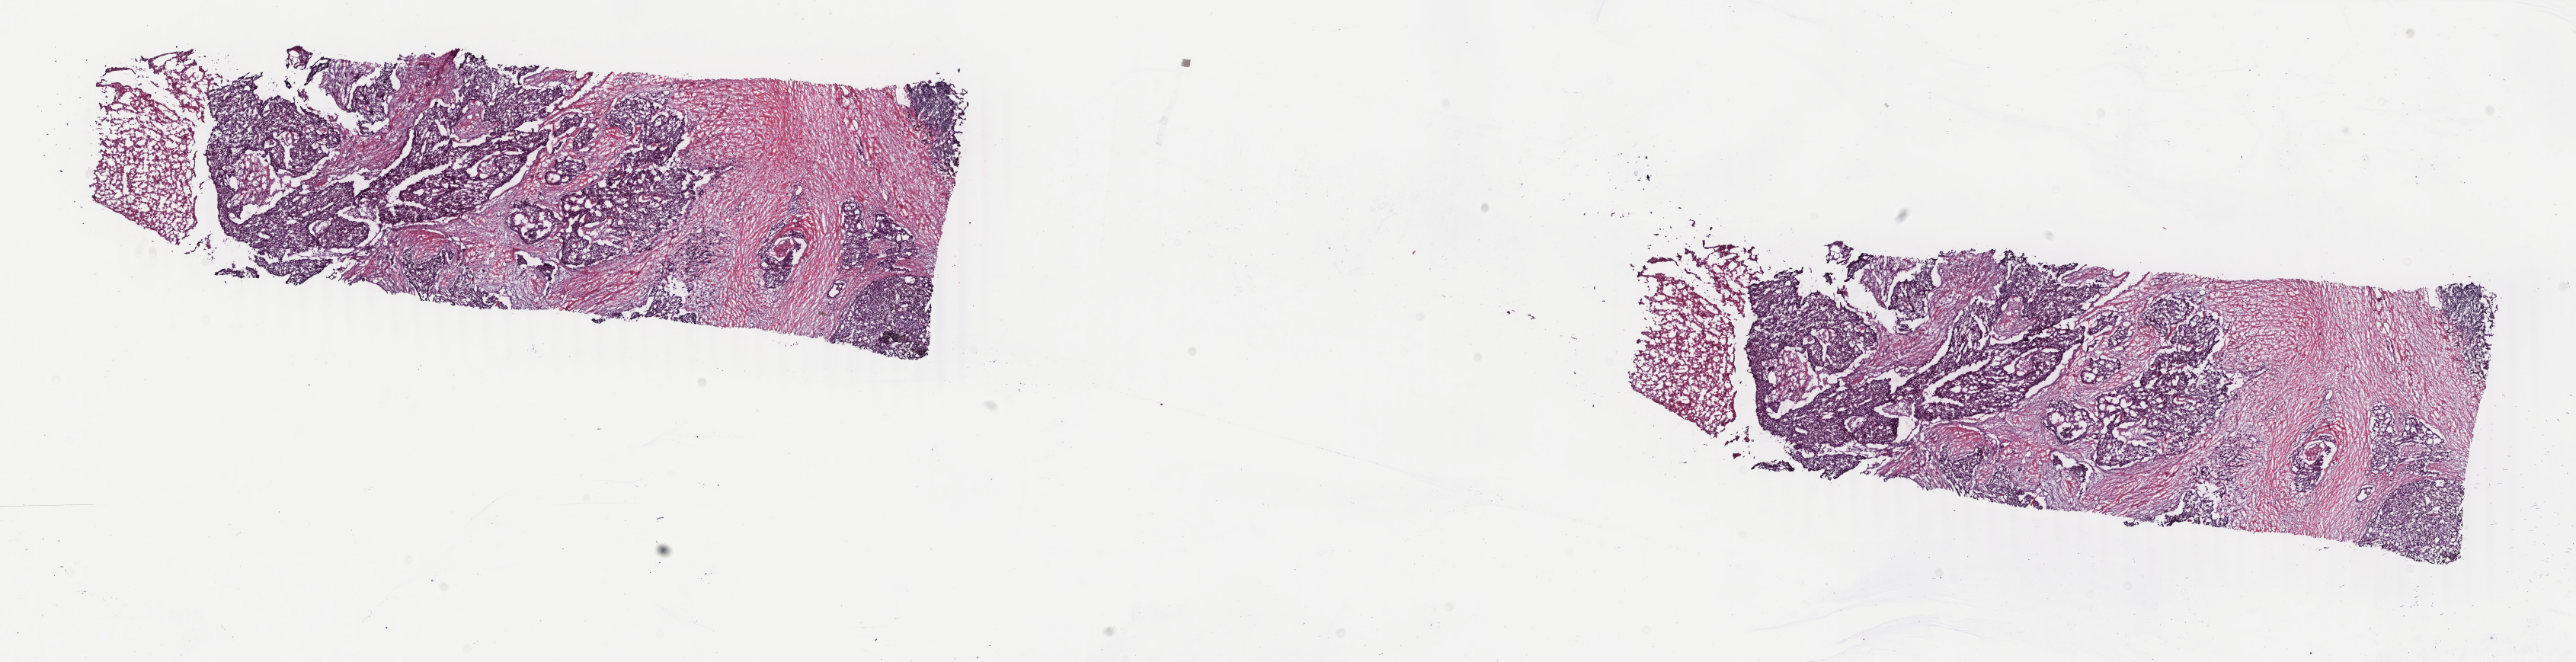
H&E-stained whole-slide image, shown as a low-resolution overview of the whole scanned area (about 26.9 x 6.9 mm). Frozen section from the top of the tissue portion. Lung, primary tumour sample. Male, age 58 years at initial diagnosis.
Diagnosis: Squamous cell carcinoma, NOS.